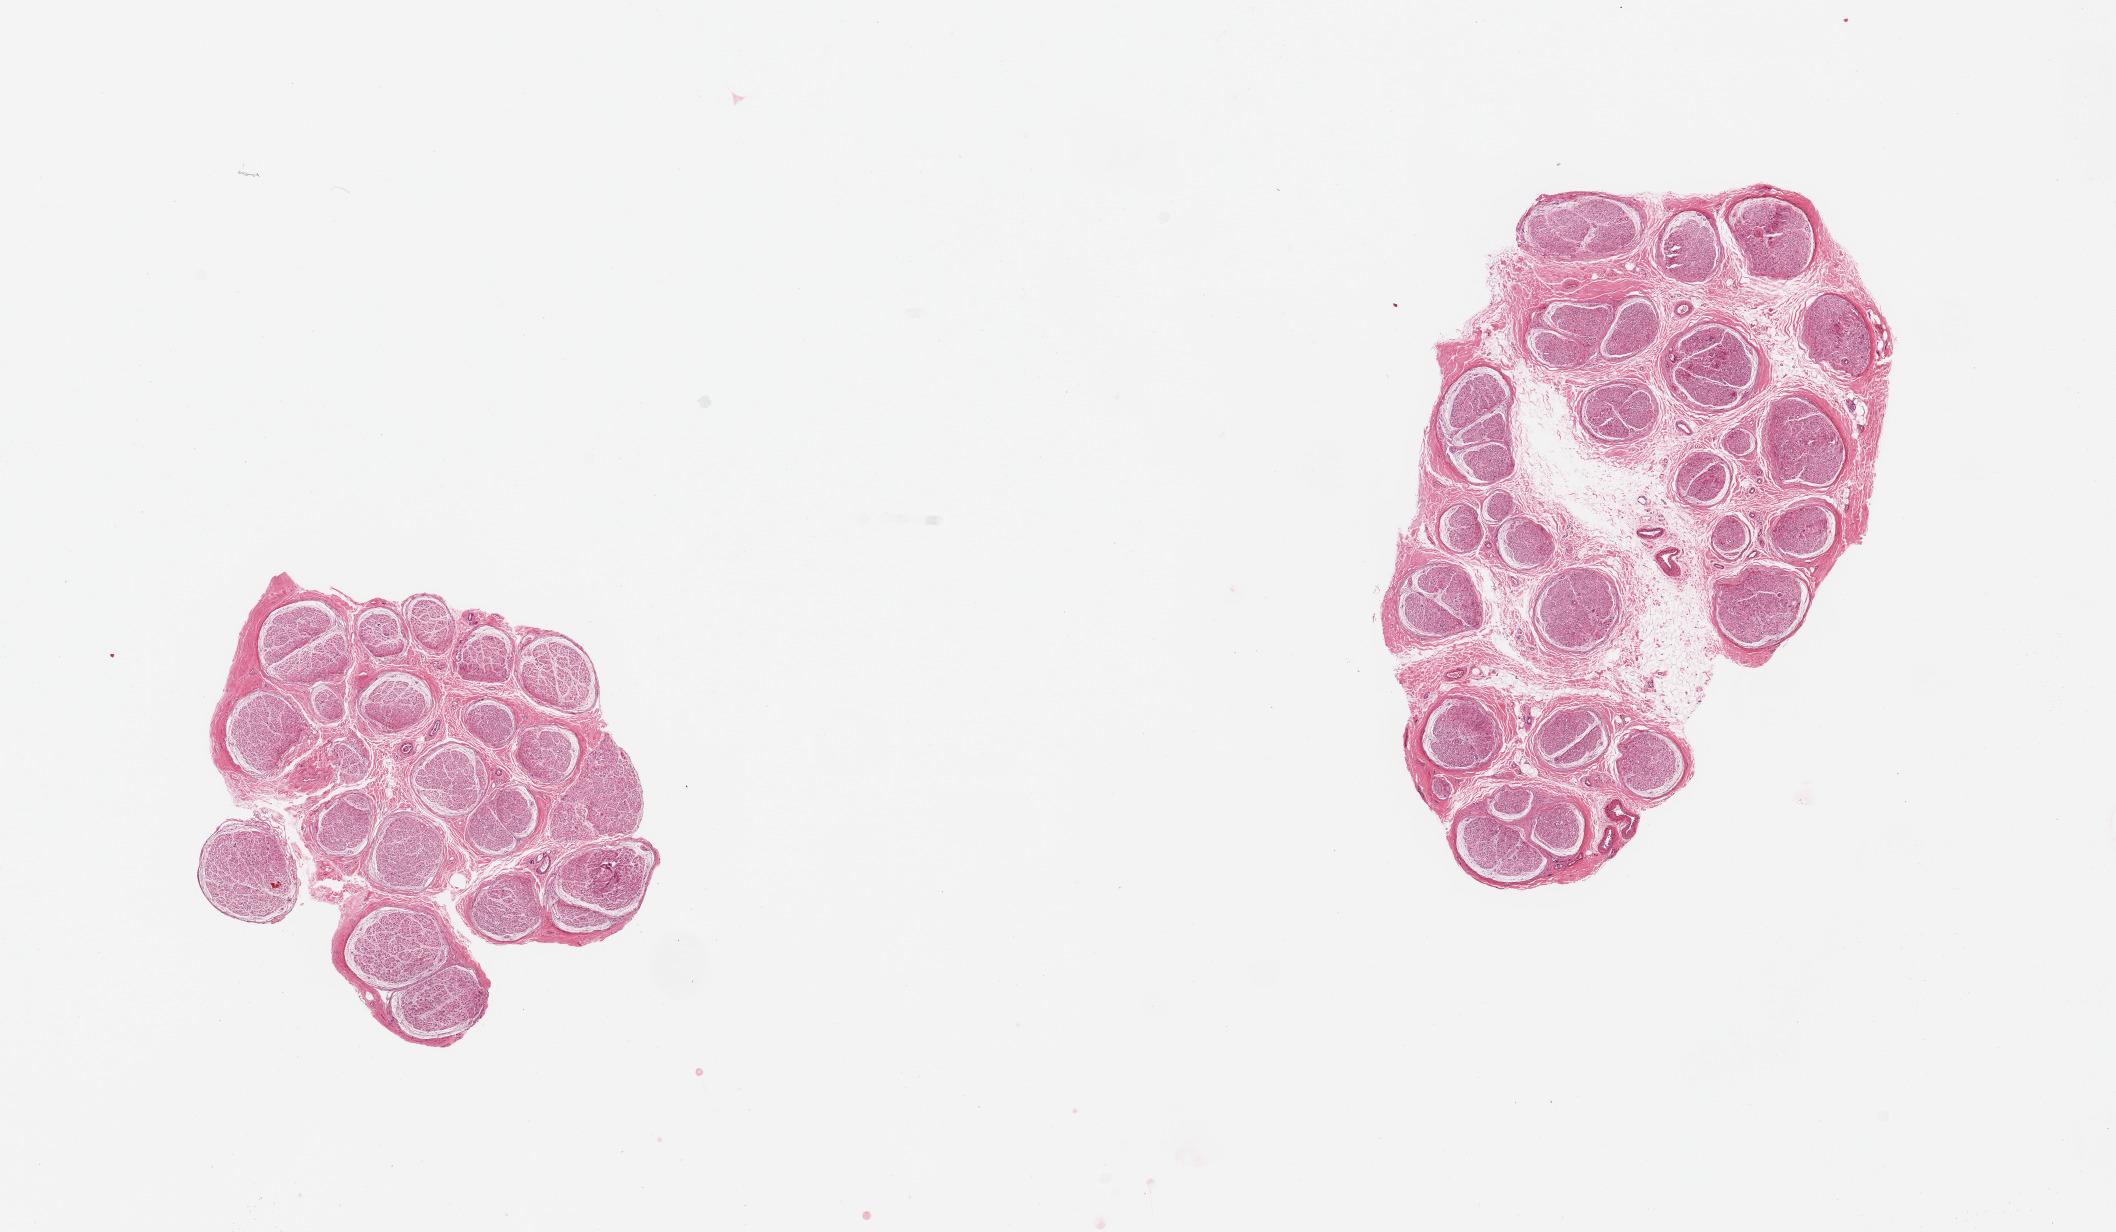
Whole-slide image, hematoxylin and eosin (H&E) stain, brightfield — low-resolution overview of the scanned area, about 16.7 x 9.7 mm. PAXgene-fixed, paraffin-embedded tissue. Target tissue: tibial nerve. Tissue donor sample. Donor sex: male.
Reviewer comment on this tissue sample: 2 pieces, no adherent fat.